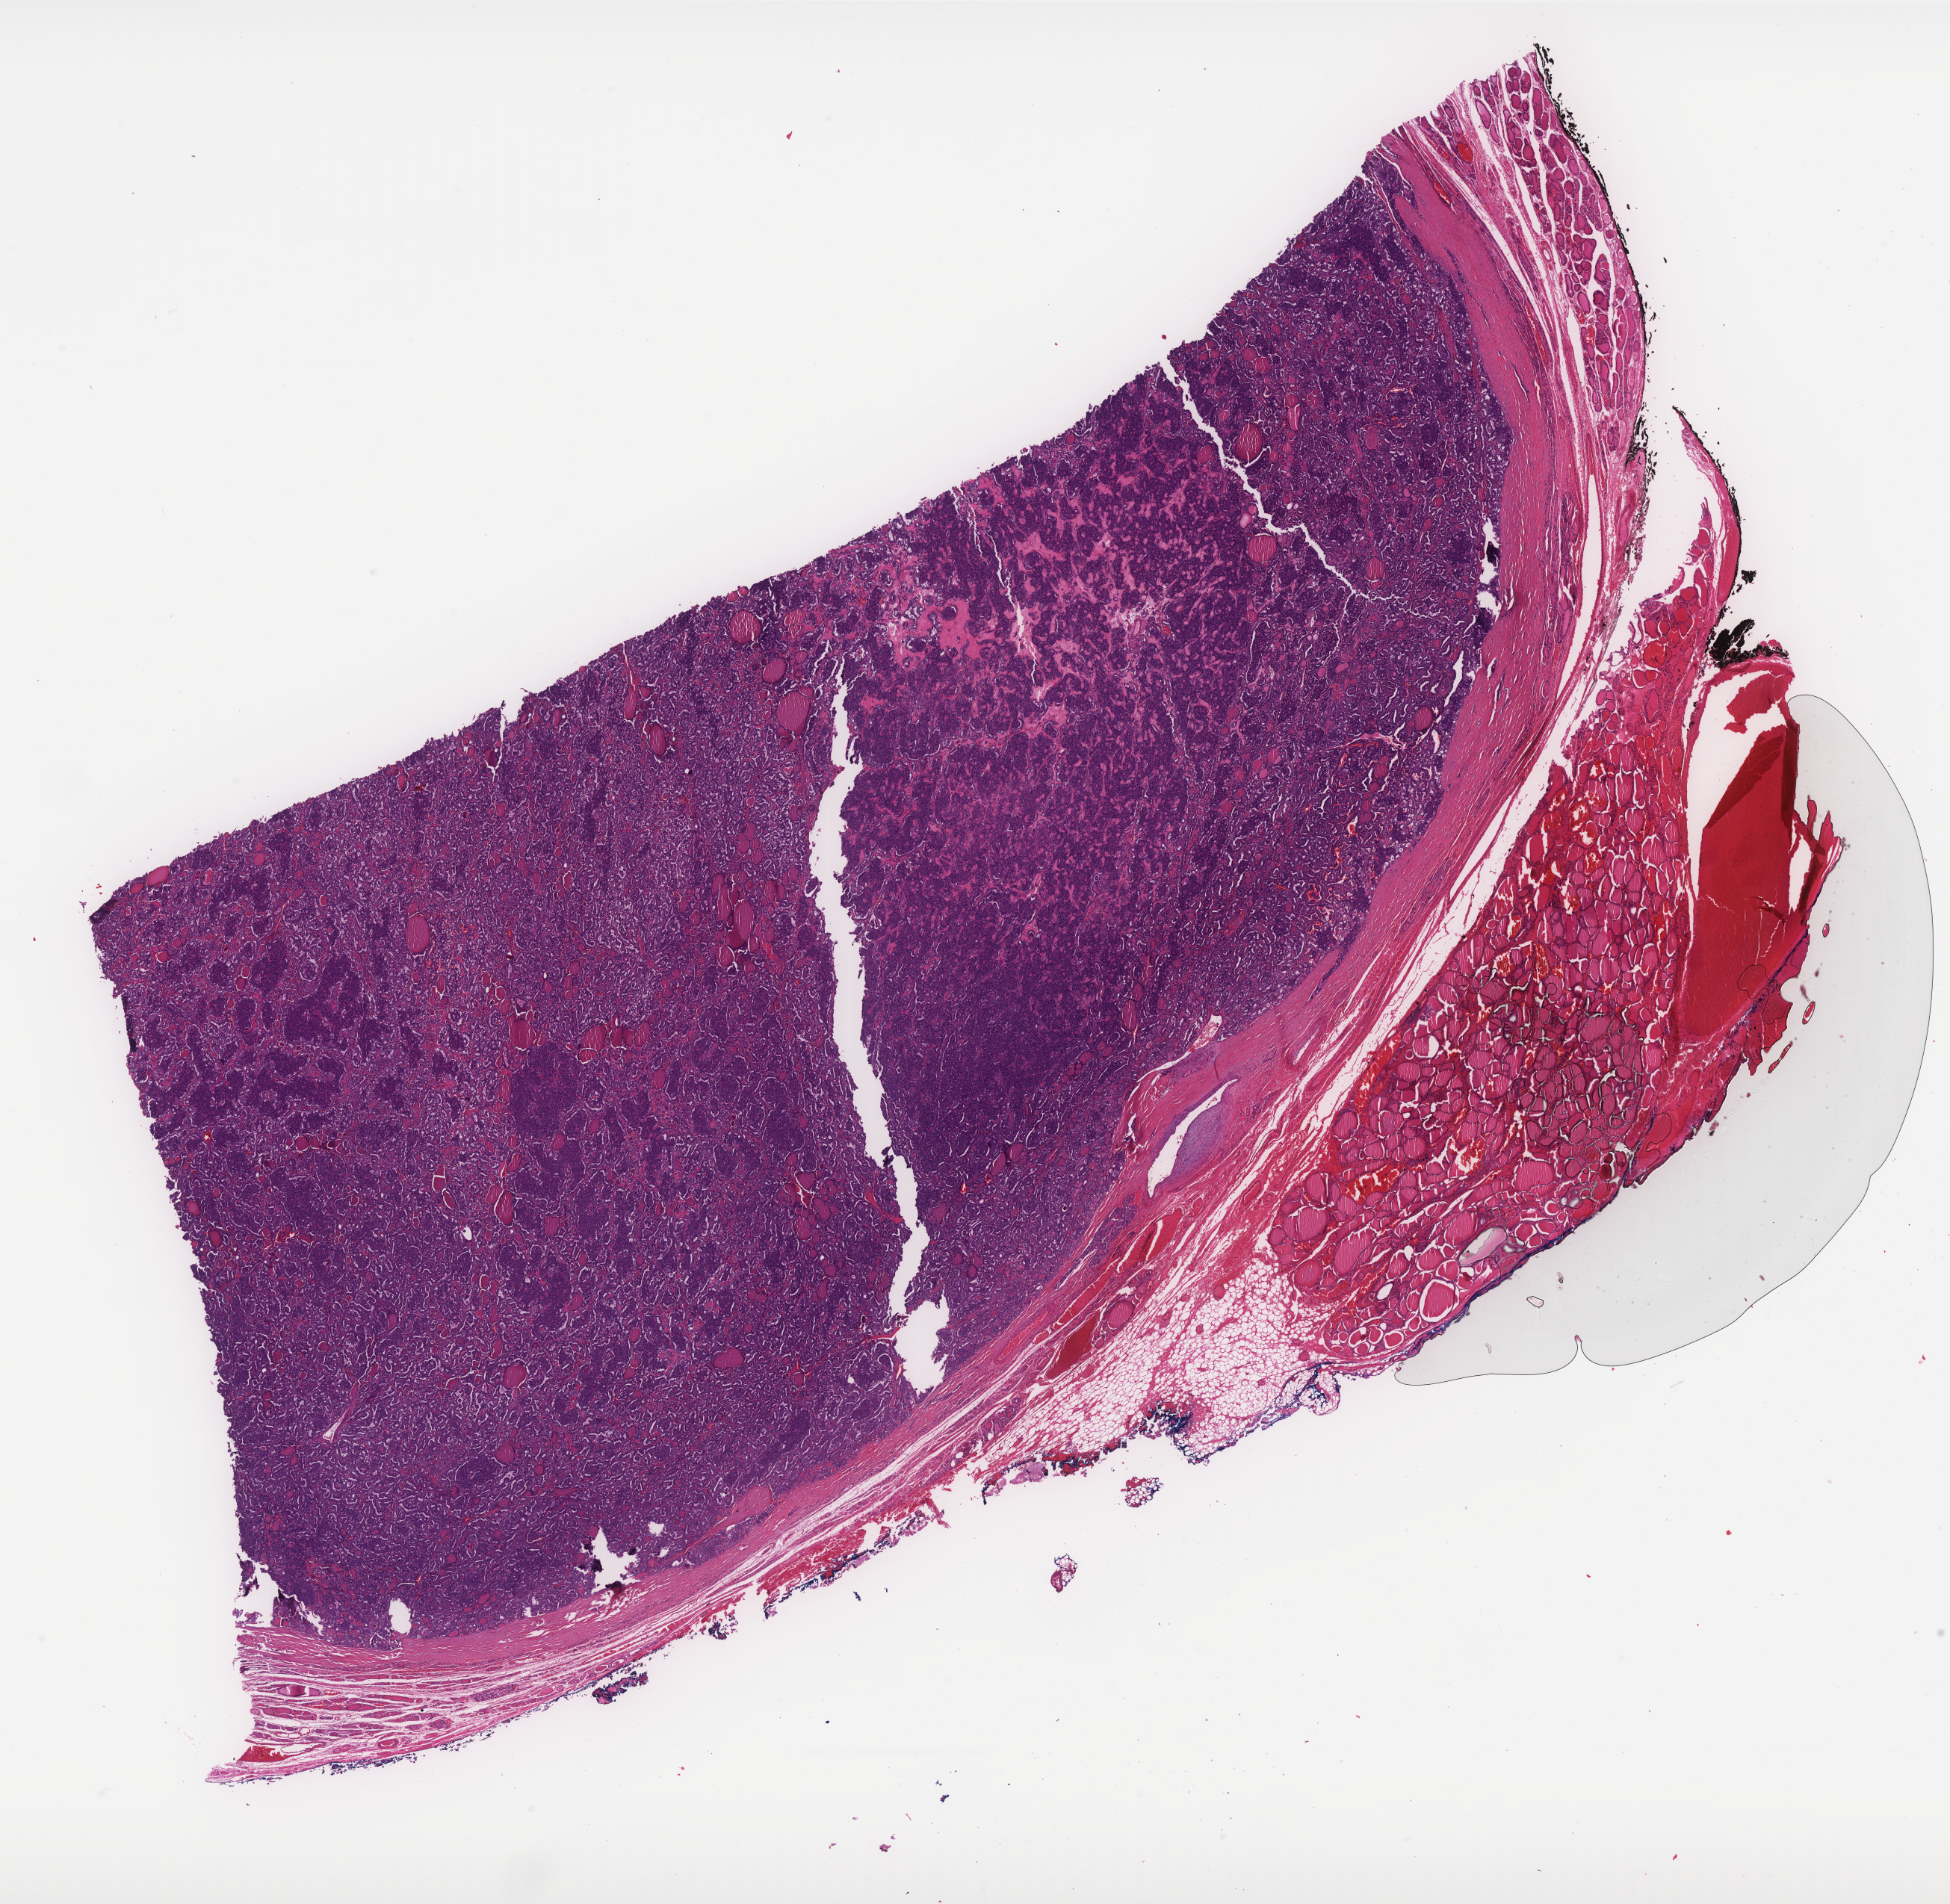
Digitized H&E-stained tissue section (whole slide), whole scanned area (about 20.9 x 20.4 mm) shown as a low-resolution overview; formalin-fixed paraffin-embedded (FFPE) diagnostic section; primary tumour sample from the thyroid. Female patient; age at initial diagnosis 23 years.
• histologic diagnosis: Papillary carcinoma, follicular variant (thyroid gland)
• AJCC pathologic stage: I
• TNM: T2 NX MX